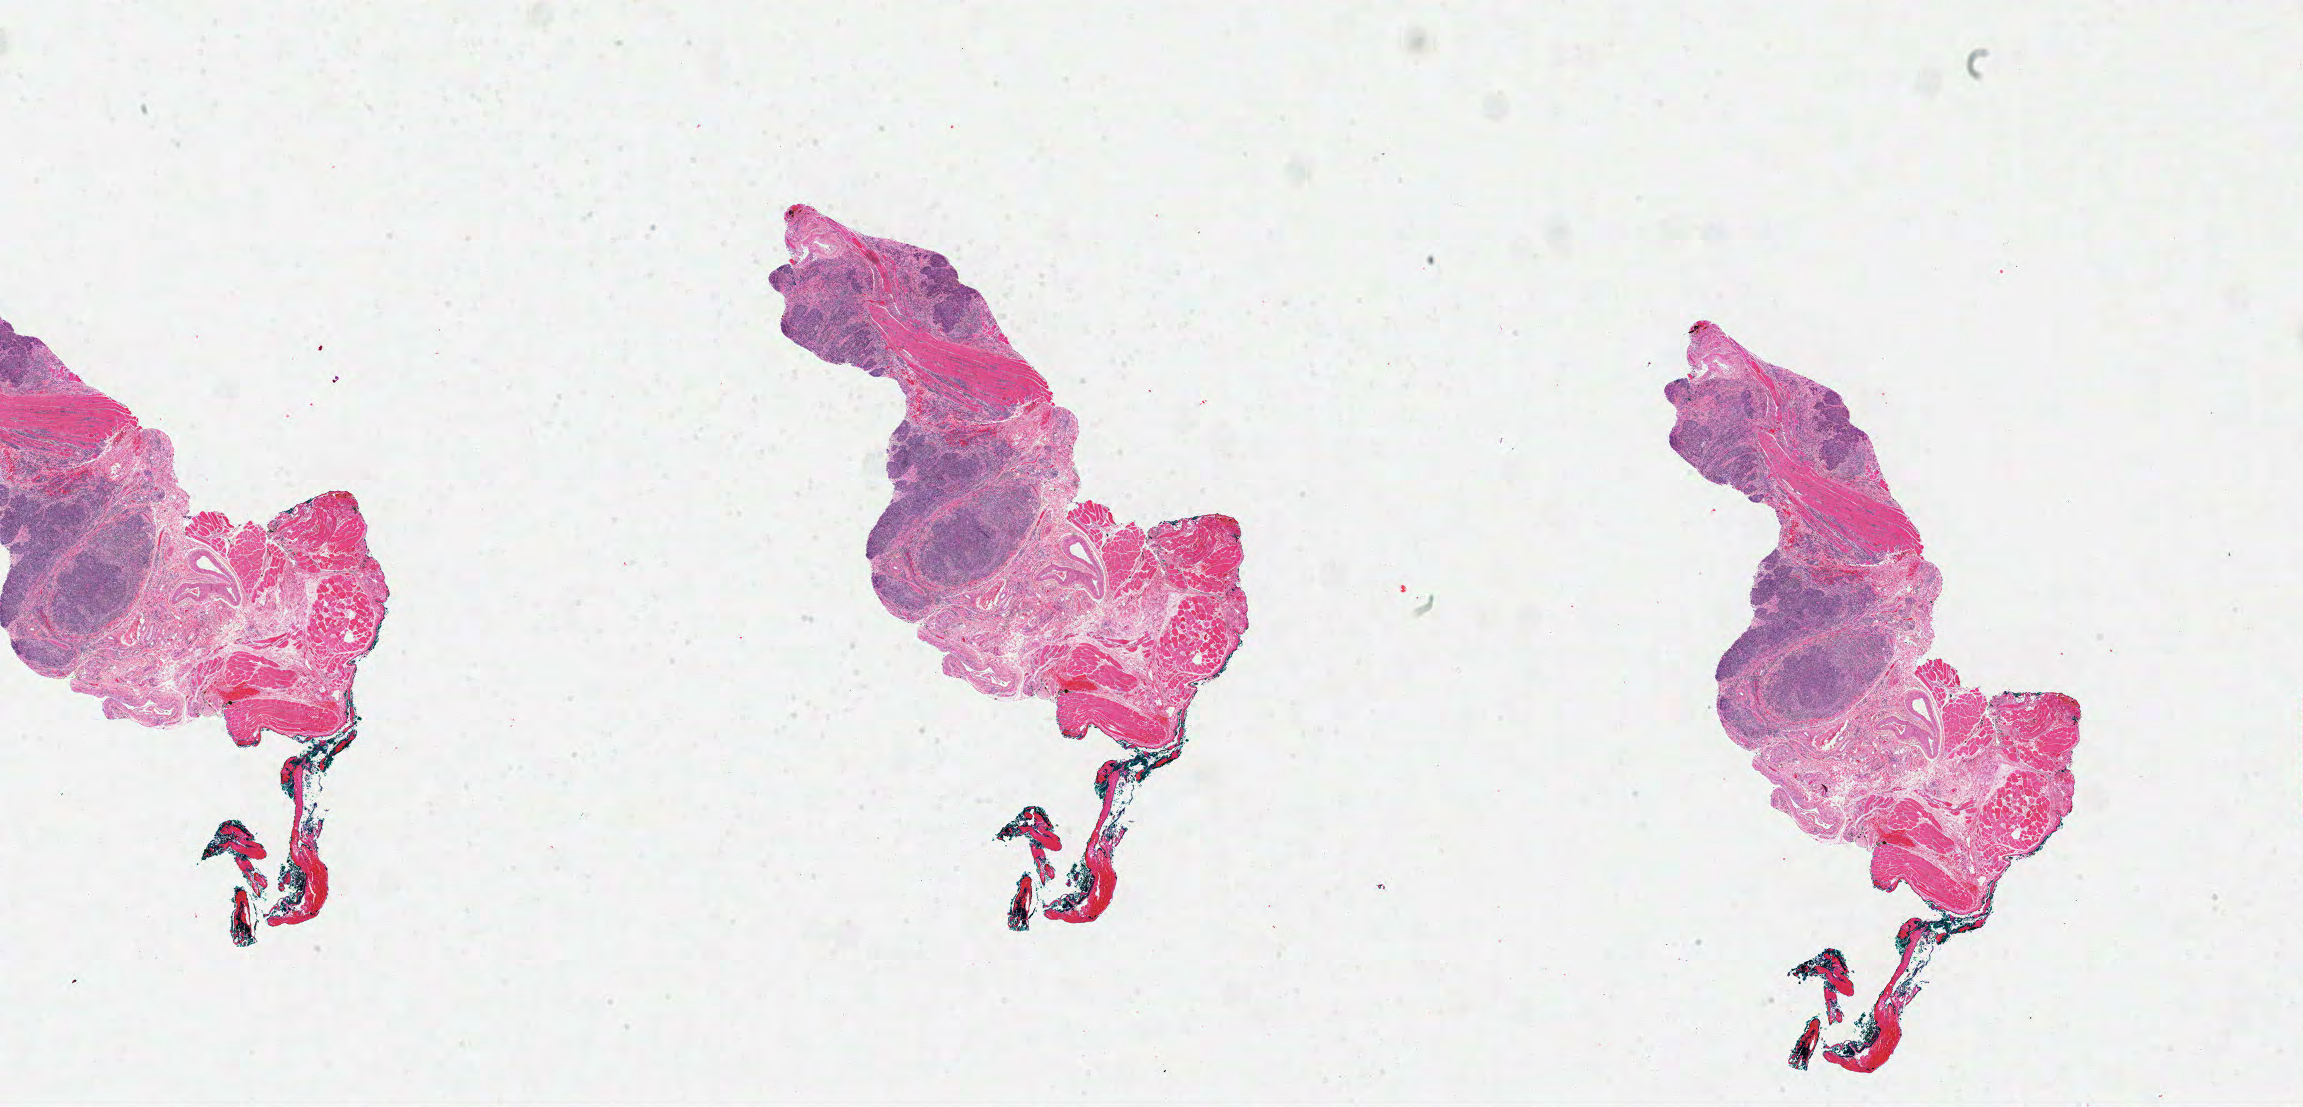
Digitized H&E tissue section (whole slide) — a low-resolution overview of the entire scanned area, about 36.2 x 17.4 mm (slide scanned at 40x), formalin-fixed paraffin-embedded (FFPE) diagnostic section, head and neck, primary tumour sample. Male, age 71 years at initial diagnosis. Histologic grade: G3 (poorly differentiated).
* lymph nodes positive (case pathology): 4 of 25 examined
* histologic diagnosis: Squamous cell carcinoma, NOS (tonsil, NOS)